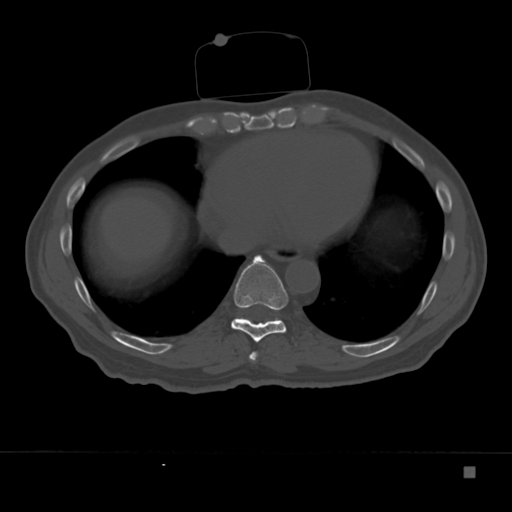
CT including the spine, one axial slice; slice 188 of 332 in the series (ordered by position); reconstruction kernel Br40s; 120 kVp; bone window (W 1800 / L 400 HU); 1.5 mm slice thickness; 512 × 512 image matrix, field of view 389 × 389 mm. Male patient, age 72 years. From the clinical record (not read from this slice): primary cancer: skeletal.
Annotated regions visible in this slice (semi-automatic segmentation, software-assisted and operator-edited):
- T8 vertebra: bounding box [x1, y1, x2, y2] px = [249, 352, 258, 361]
- T9 vertebra: [231, 255, 288, 343]